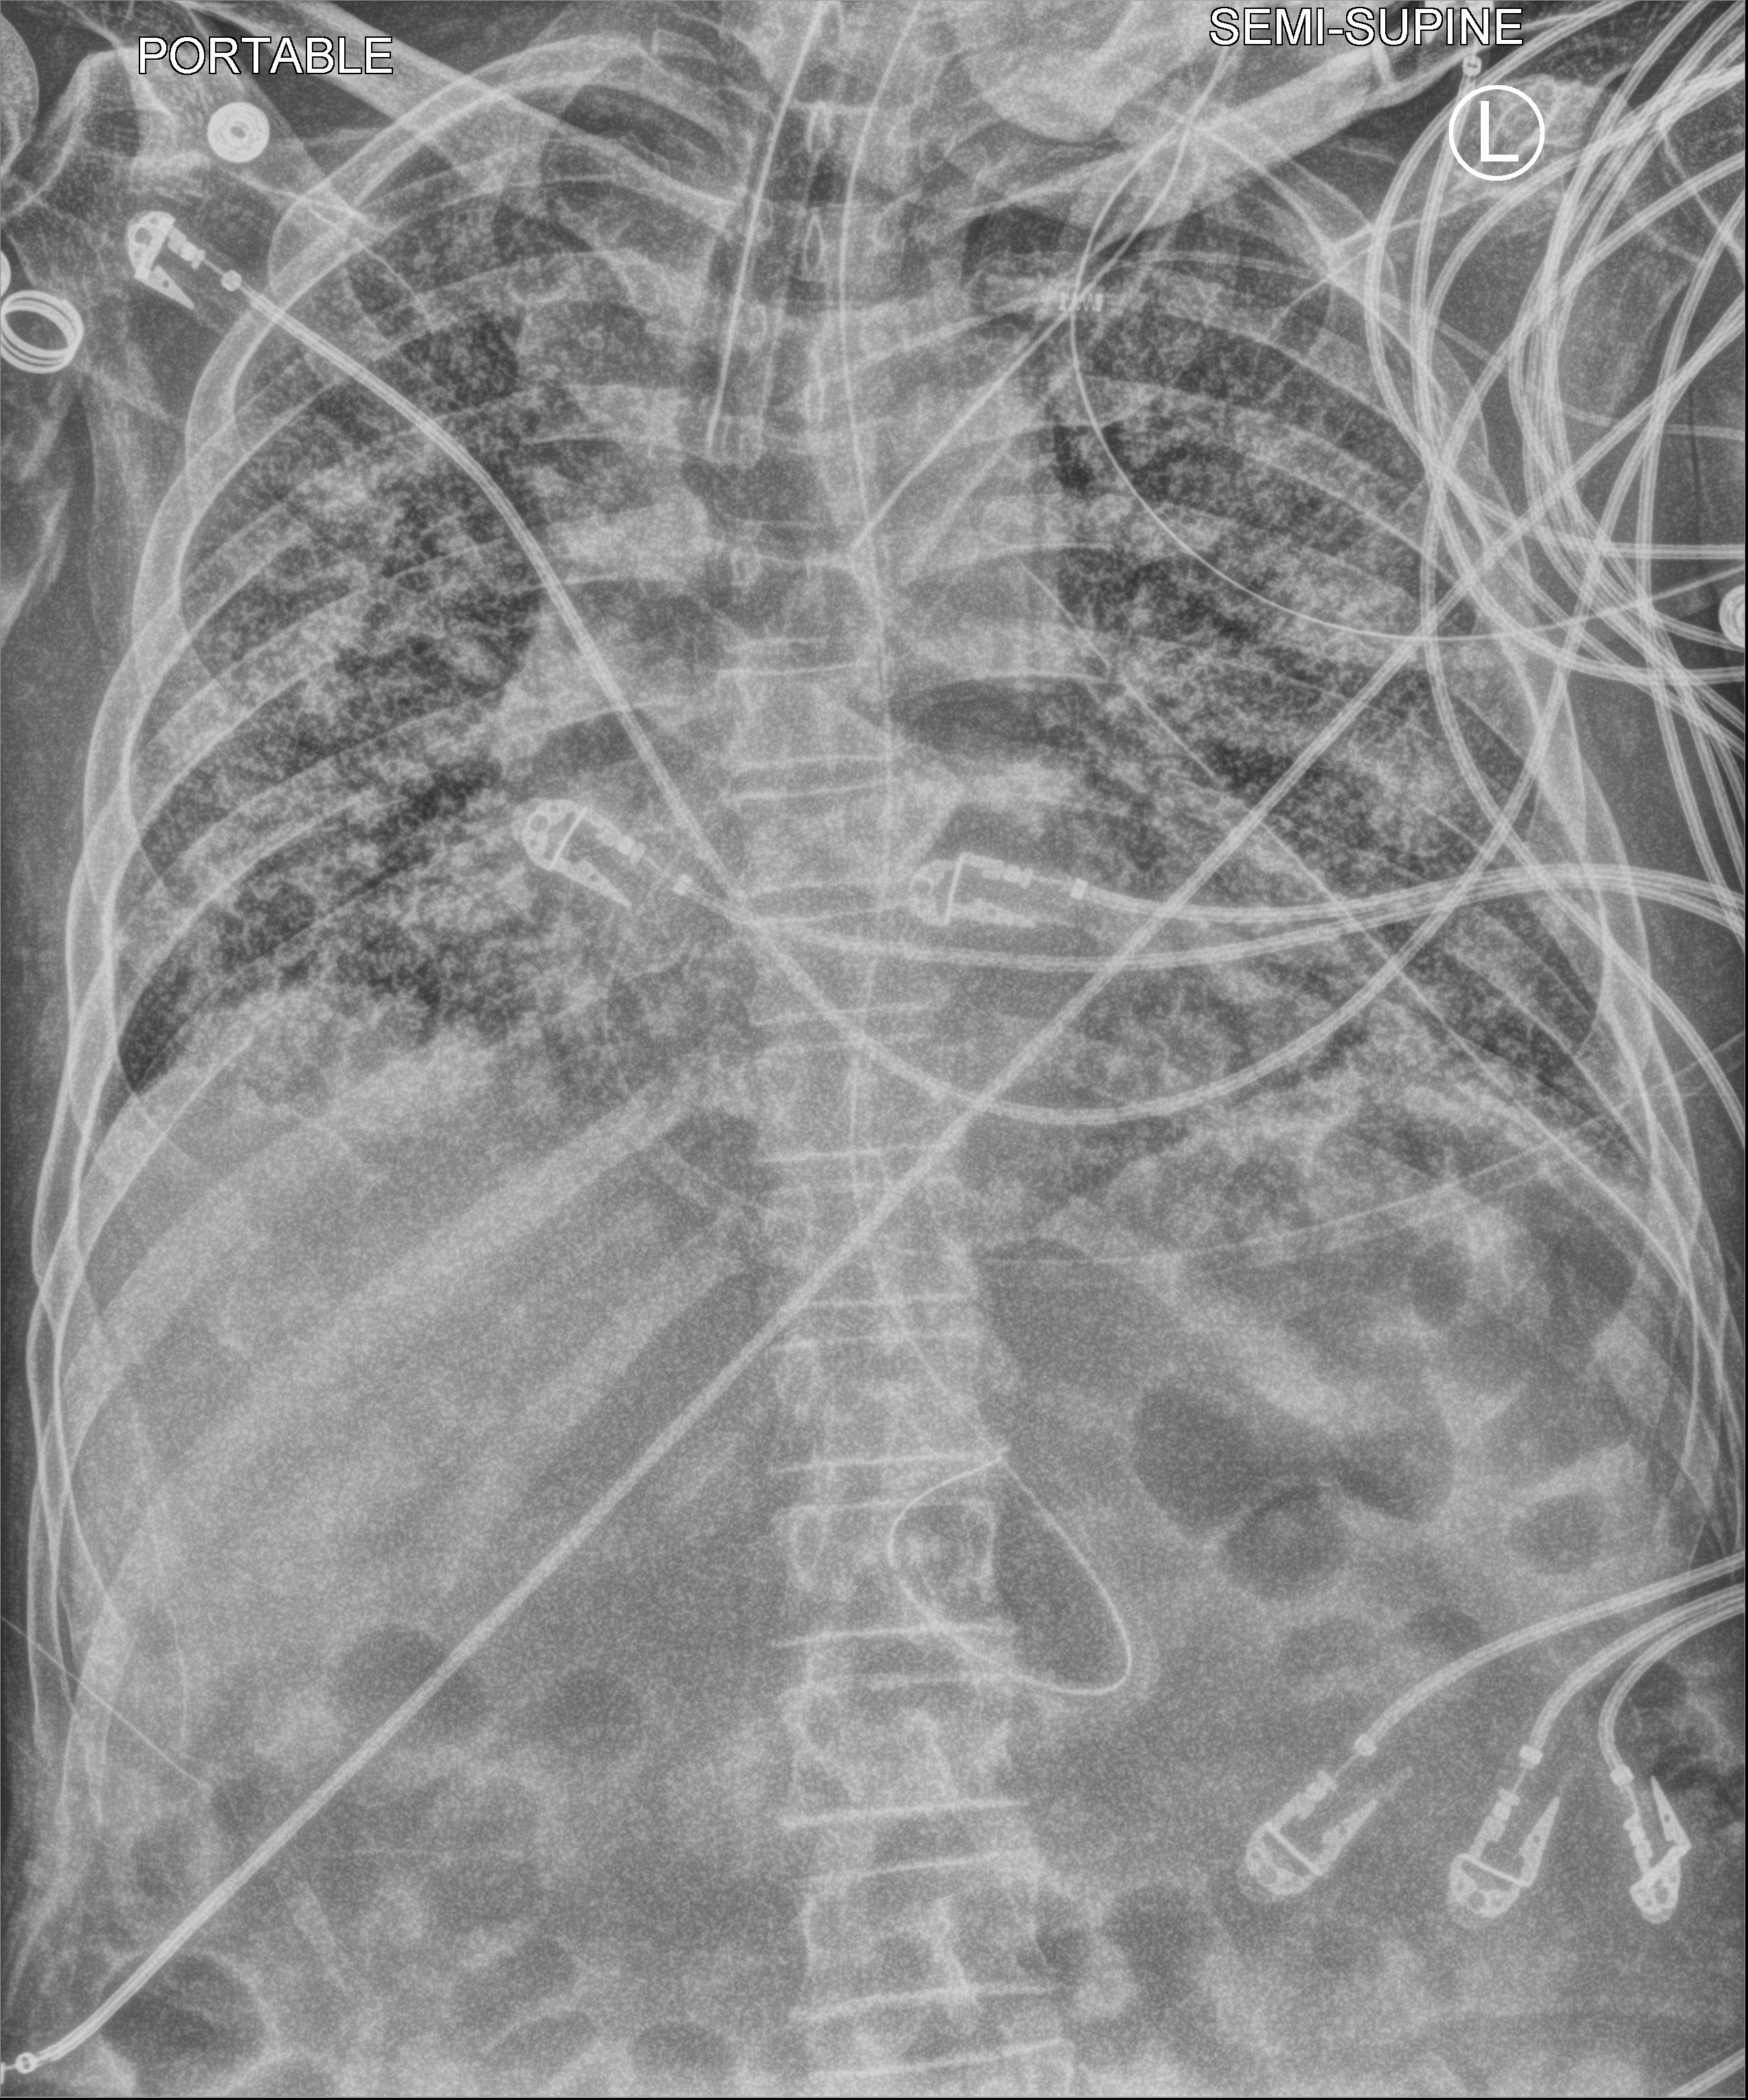
Portable chest radiograph; anteroposterior (AP) projection. Male patient hospitalised with COVID-19, age 60–74 years.
From the hospital-stay record, not from the radiograph (when in the stay this image was taken is not recorded):
- admitted to intensive care during this hospital stay: yes
- mechanically ventilated during this hospital stay: yes